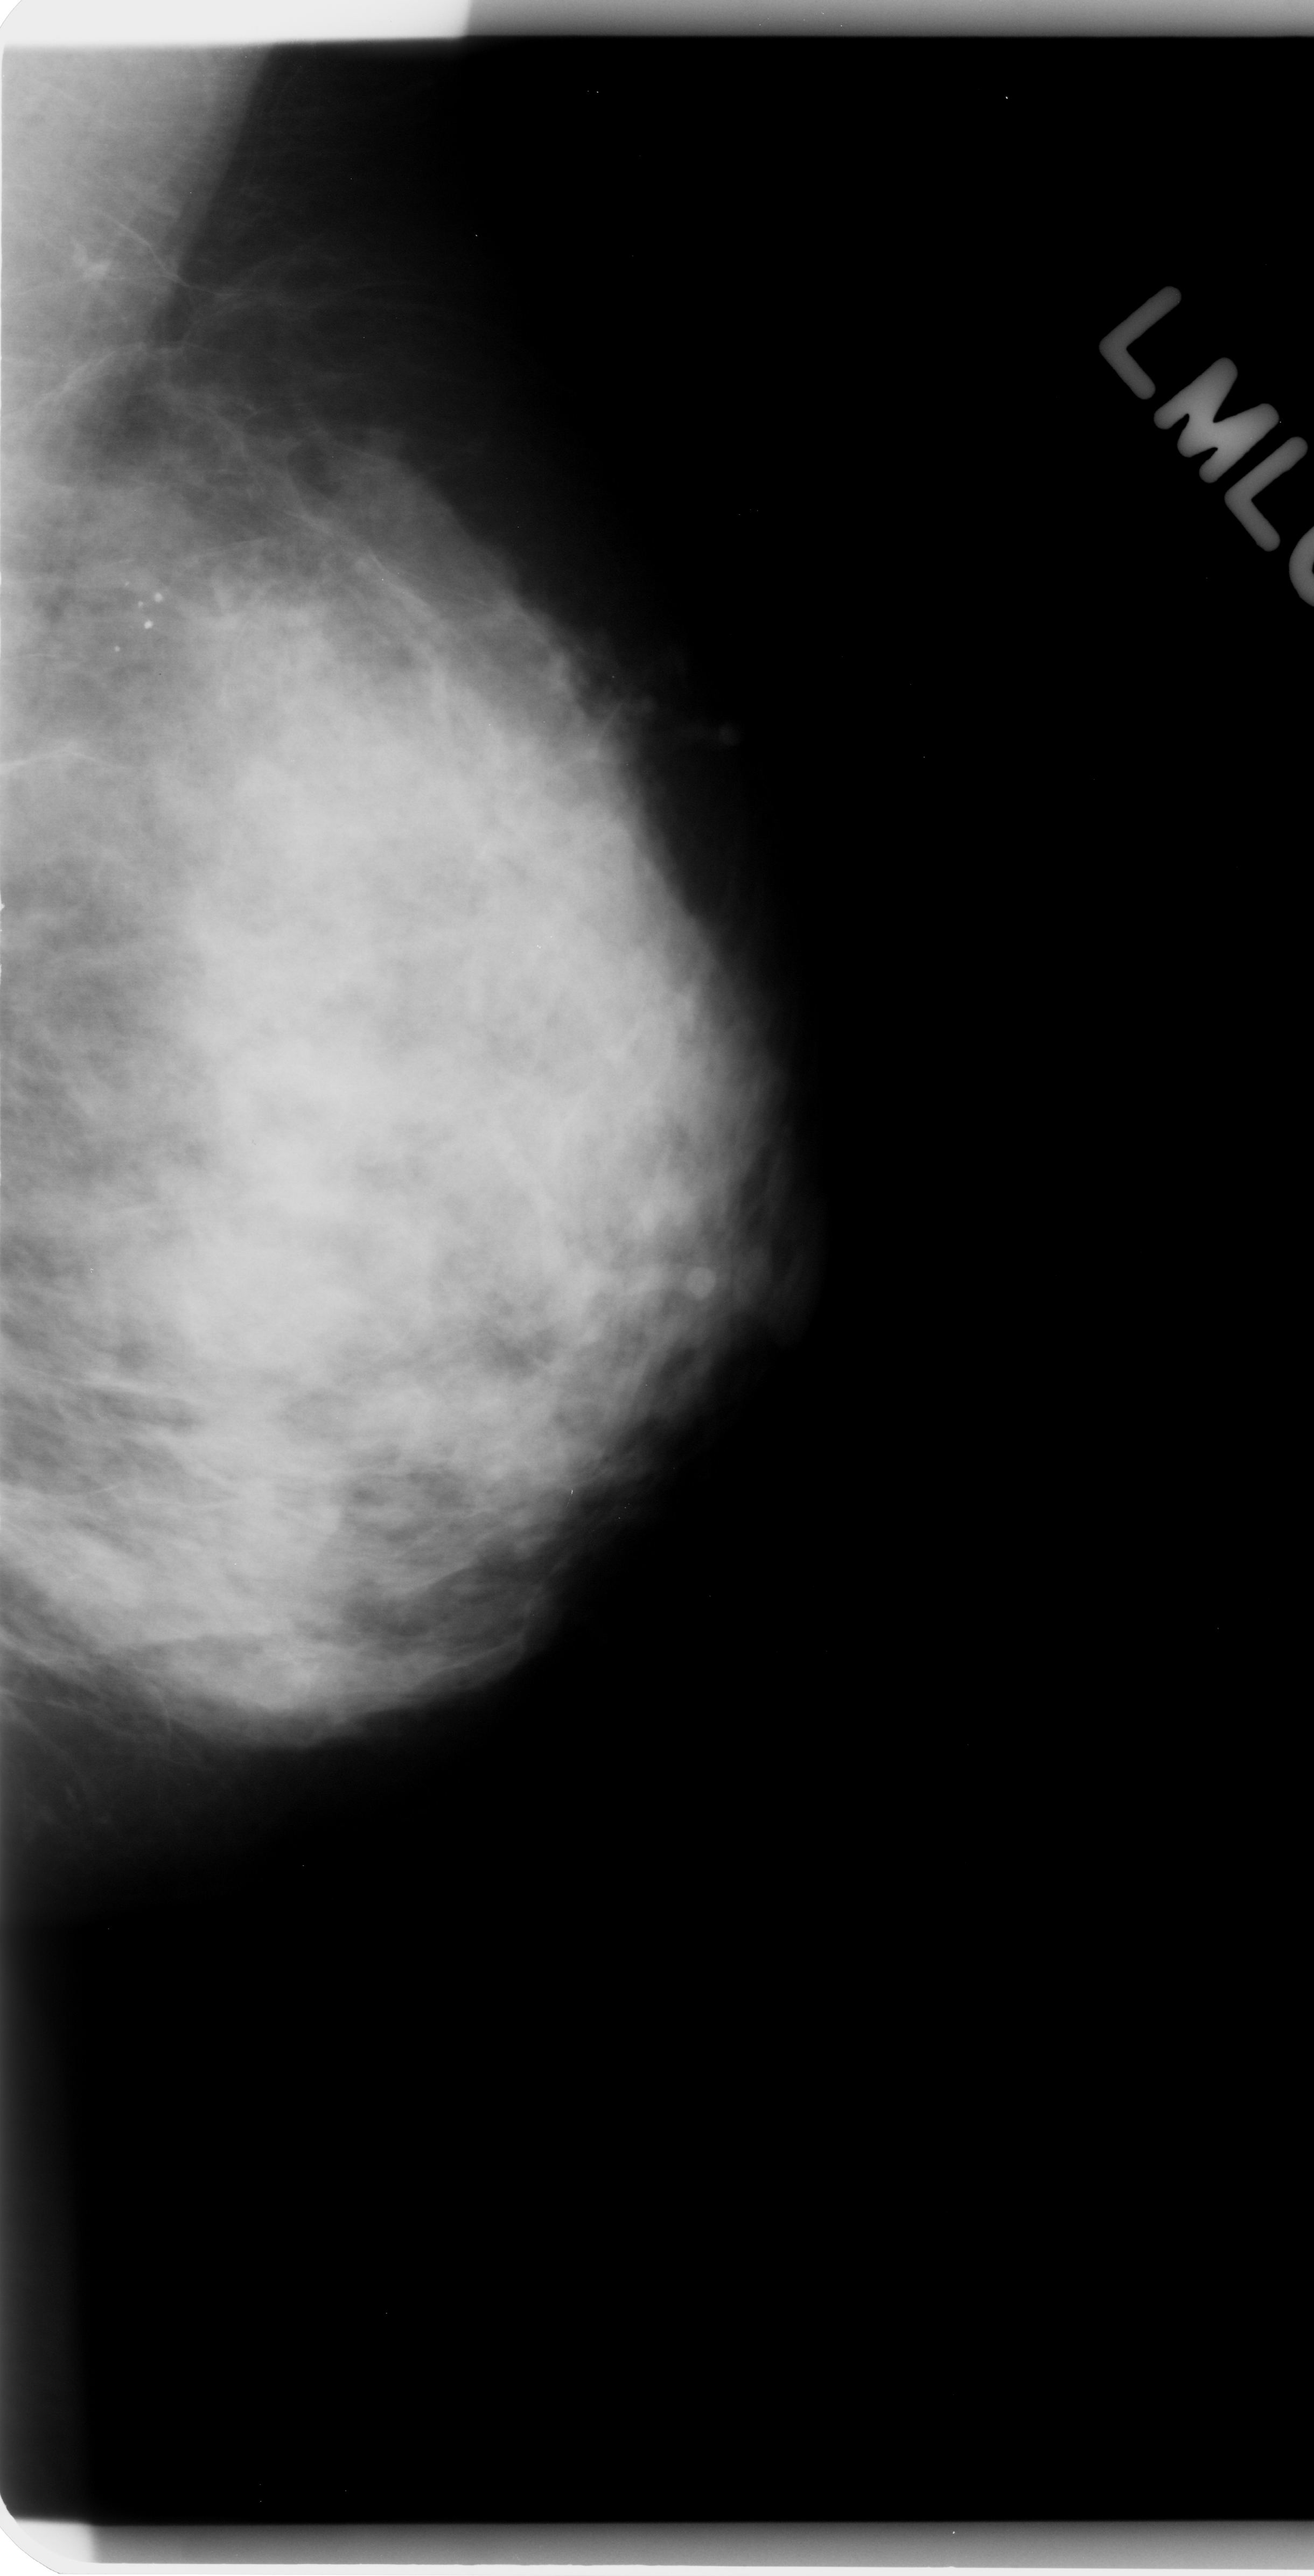
Digitized screen-film mammogram, left breast, mediolateral oblique (MLO) view, breast composition: heterogeneously dense (BI-RADS density category 3 of 4).
Marked abnormality: calcifications, morphology pleomorphic, distribution clustered; BI-RADS assessment category 4; pathology result (as recorded, not read from the image): benign.